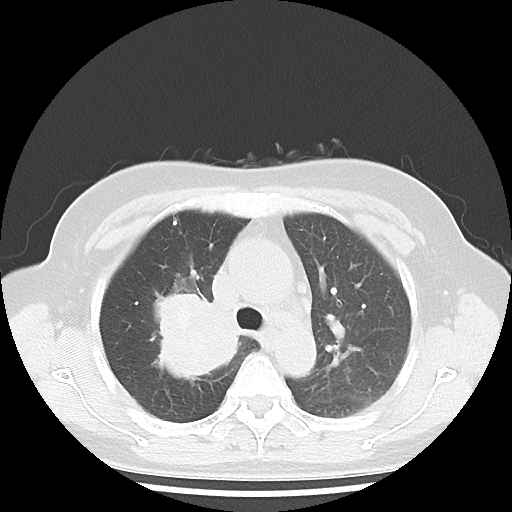
Chest CT, one axial slice; slice 29 of 43 in the series (ordered by position); 100 kVp; lung window (W 1500 / L -600 HU); 5 mm slice thickness; 512 × 512 image matrix, field of view 316 × 316 mm. Female patient, age 62 years. From the clinical record (not read from this slice): clinical TNM (as recorded): T3 N0 M0; histopathological grade: G3.
Structures marked on this image (rectangle marked by the reading radiologist):
- lung tumour (recorded histology: small cell carcinoma): bounding box <135,277,248,389> (left, top, right, bottom; pixels)